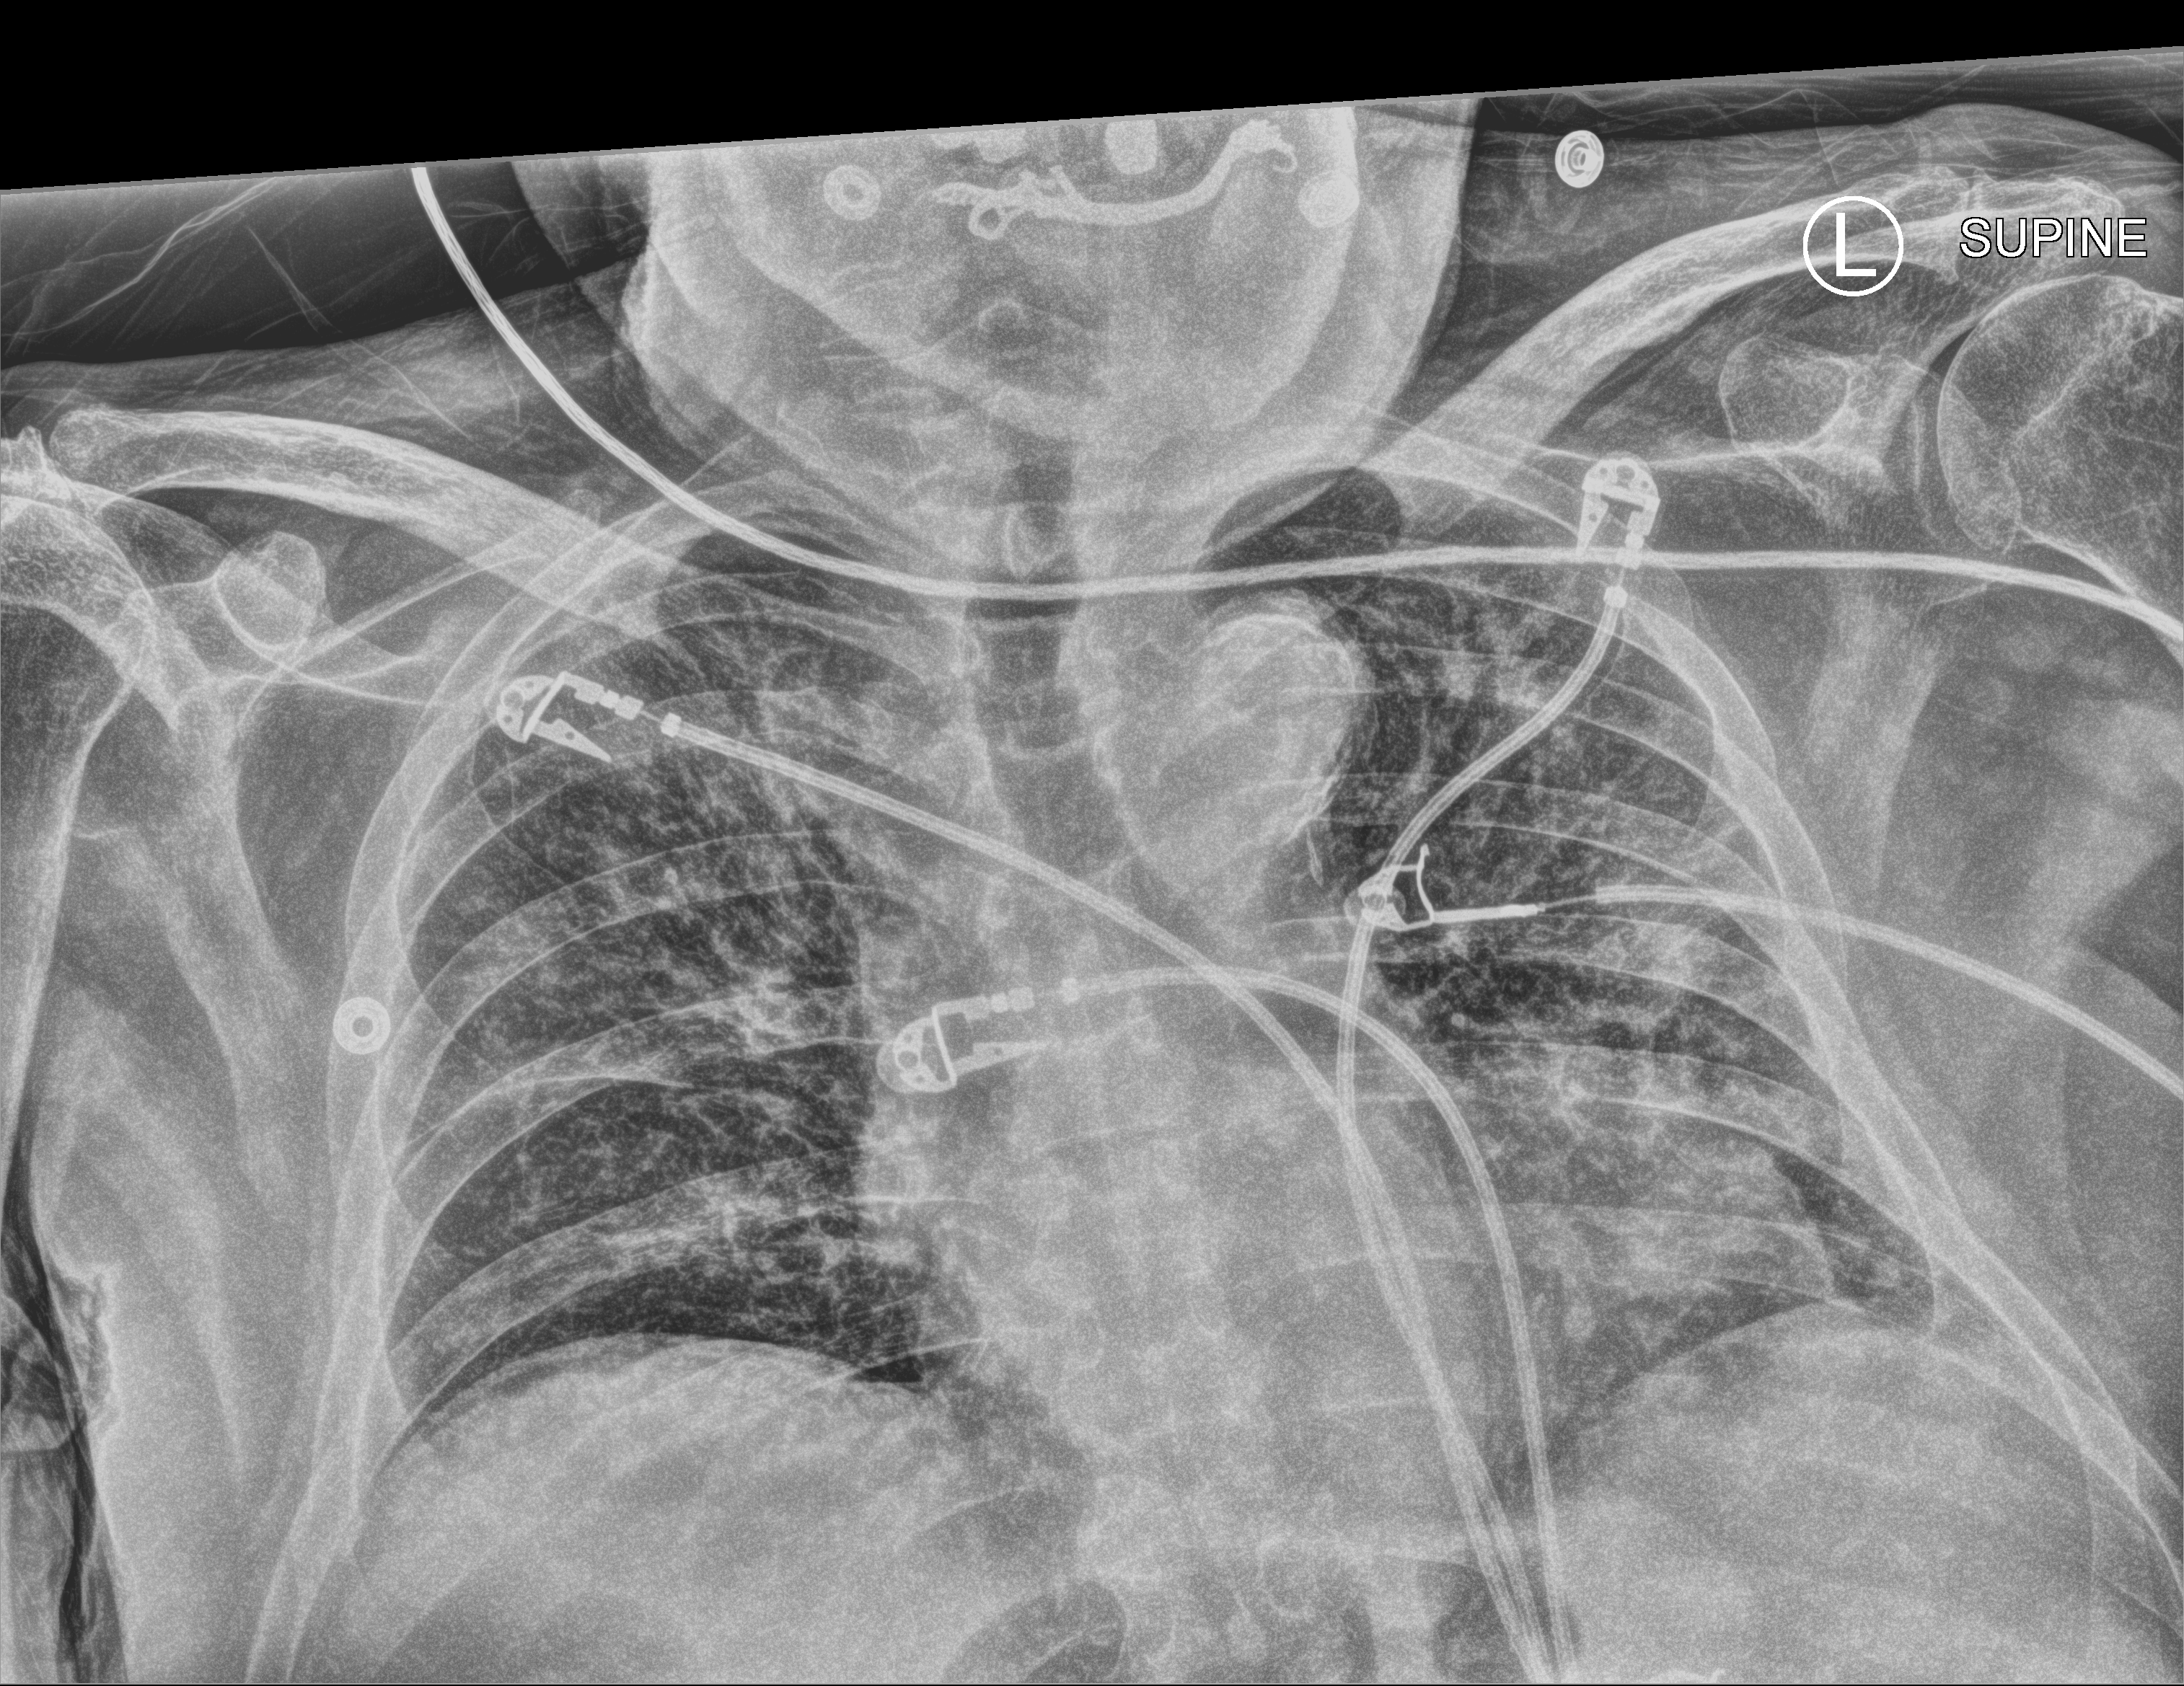
Bedside chest radiograph (computed radiography), anteroposterior (AP) projection. Patient hospitalised with COVID-19; male, aged 75–90 years.
Hospital-stay facts (about this admission, not read from this image; timing relative to this image not recorded): mechanically ventilated during this hospital stay: no; length of hospital stay: 8 days.